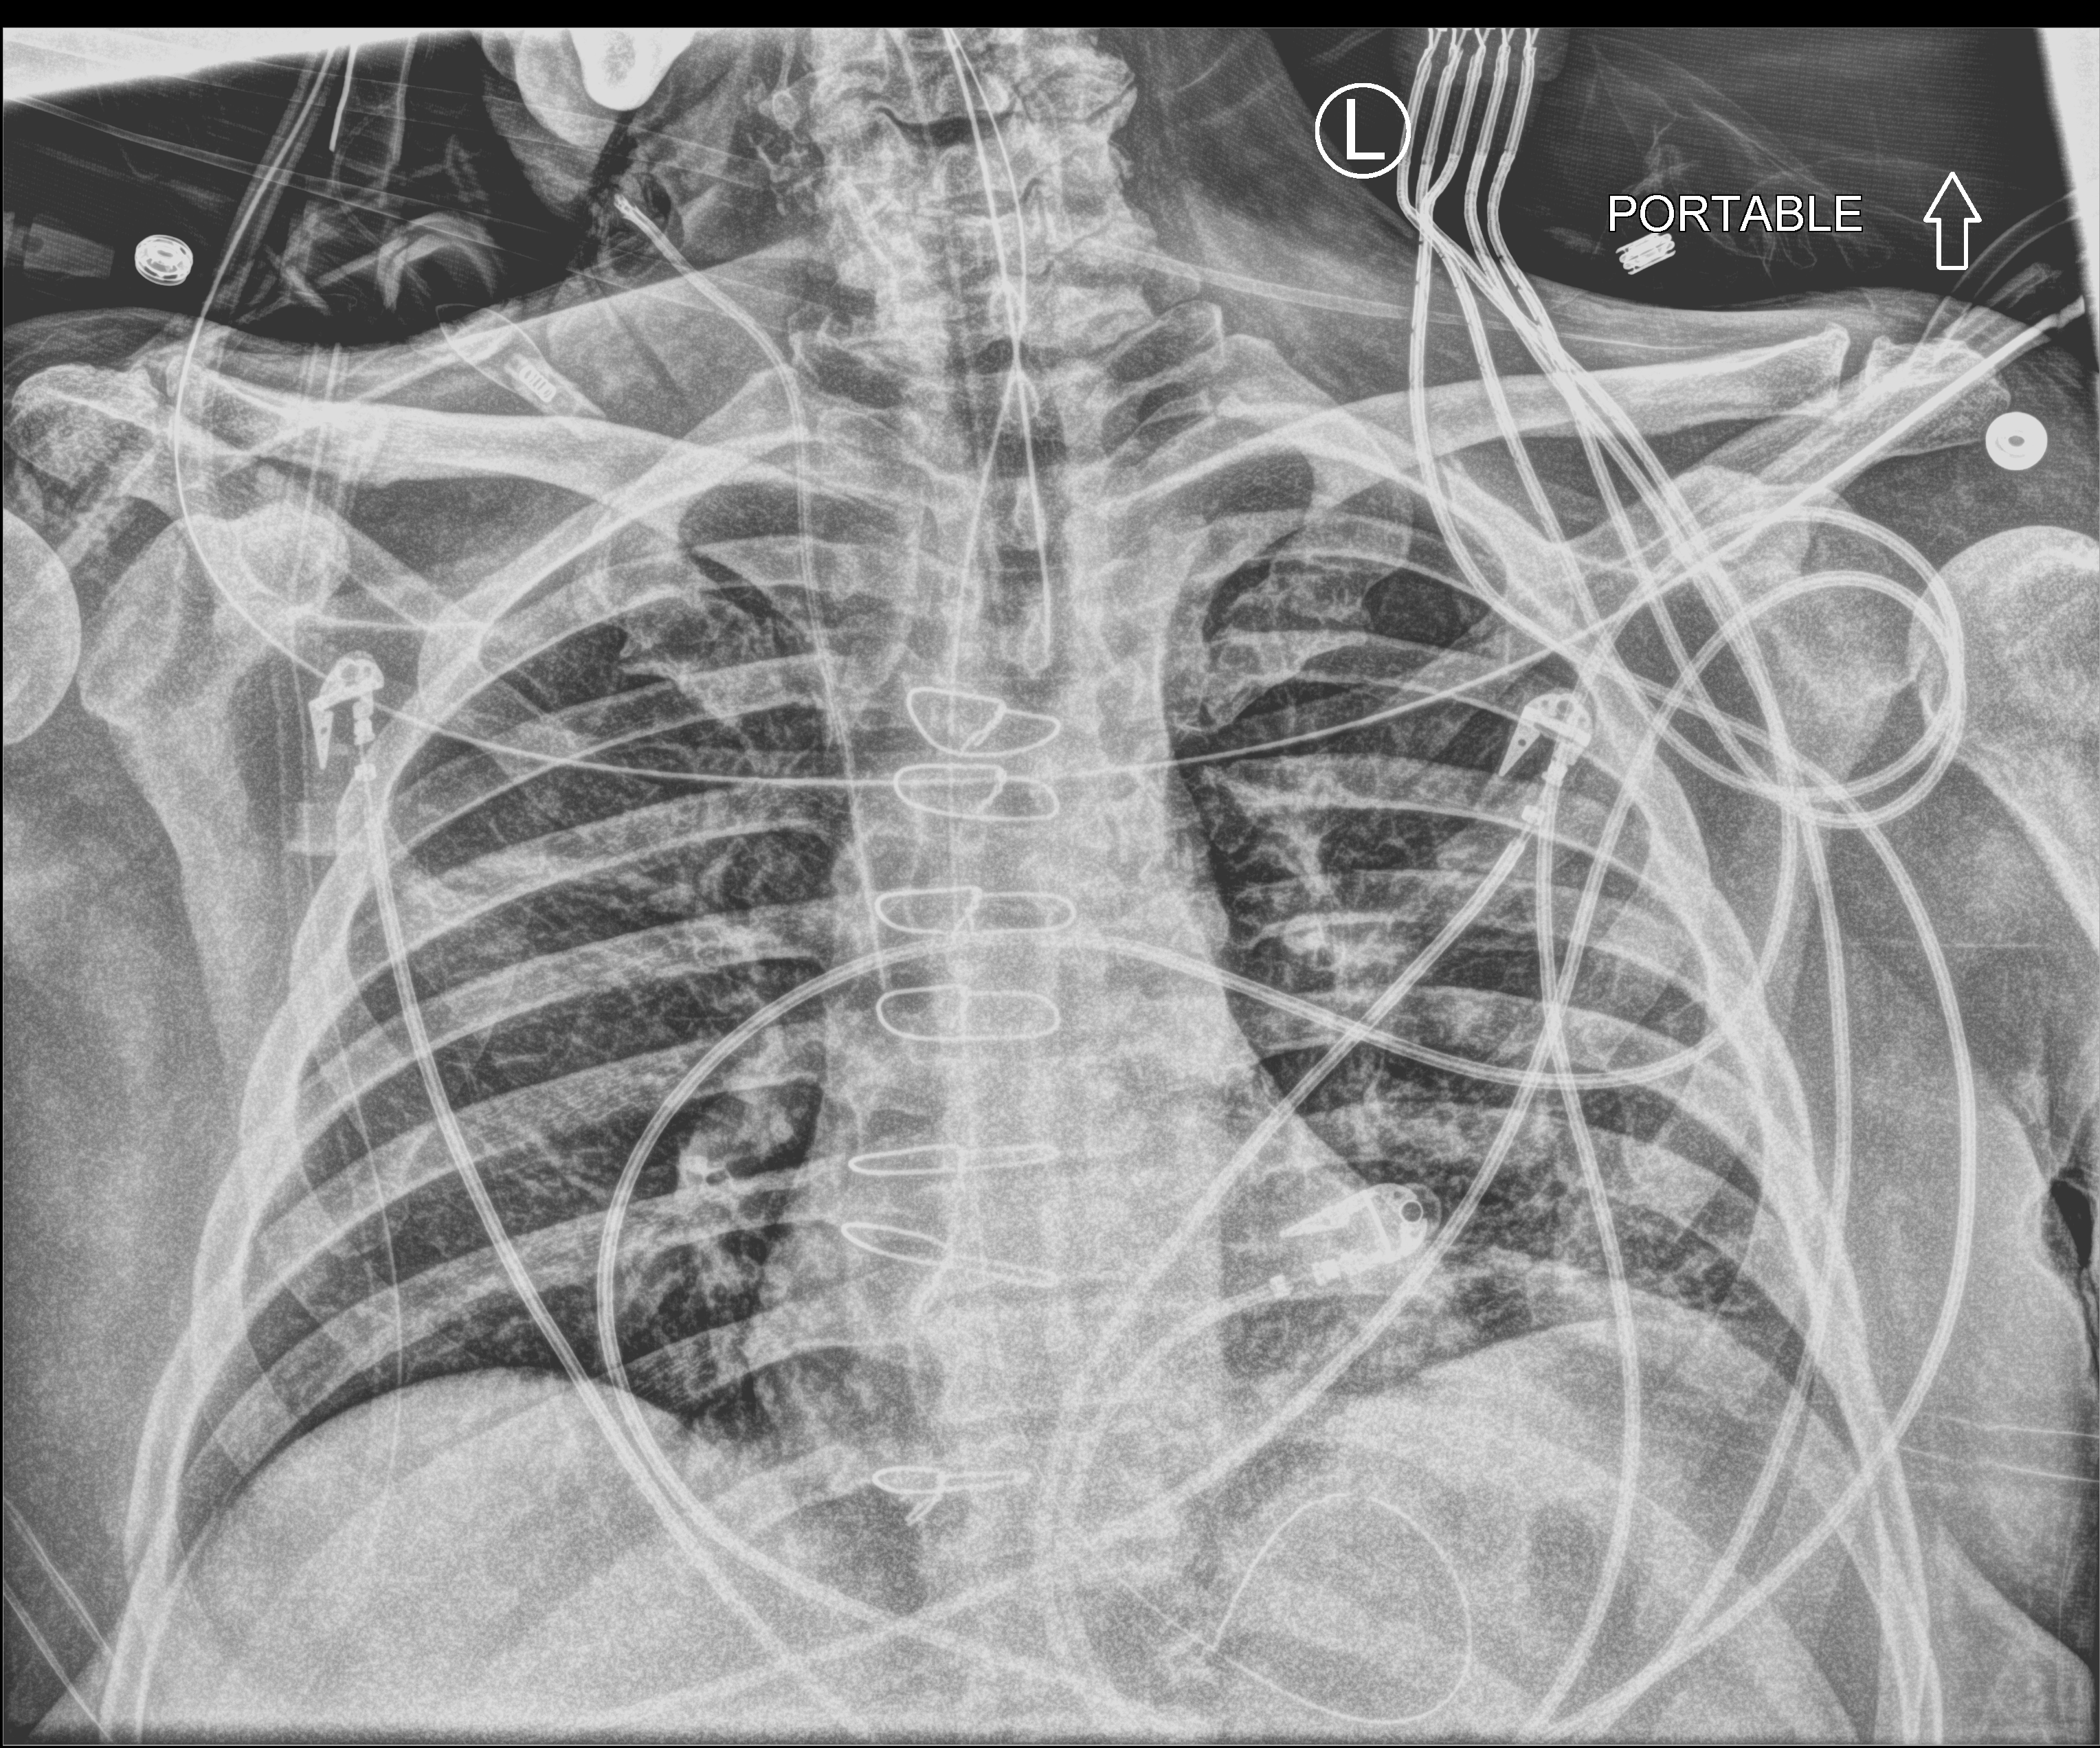
Portable chest radiograph. Male patient hospitalised with COVID-19, age 60–74 years.
From the hospital-stay record, not from the radiograph (when in the stay this image was taken is not recorded): admitted to intensive care during this hospital stay: yes.